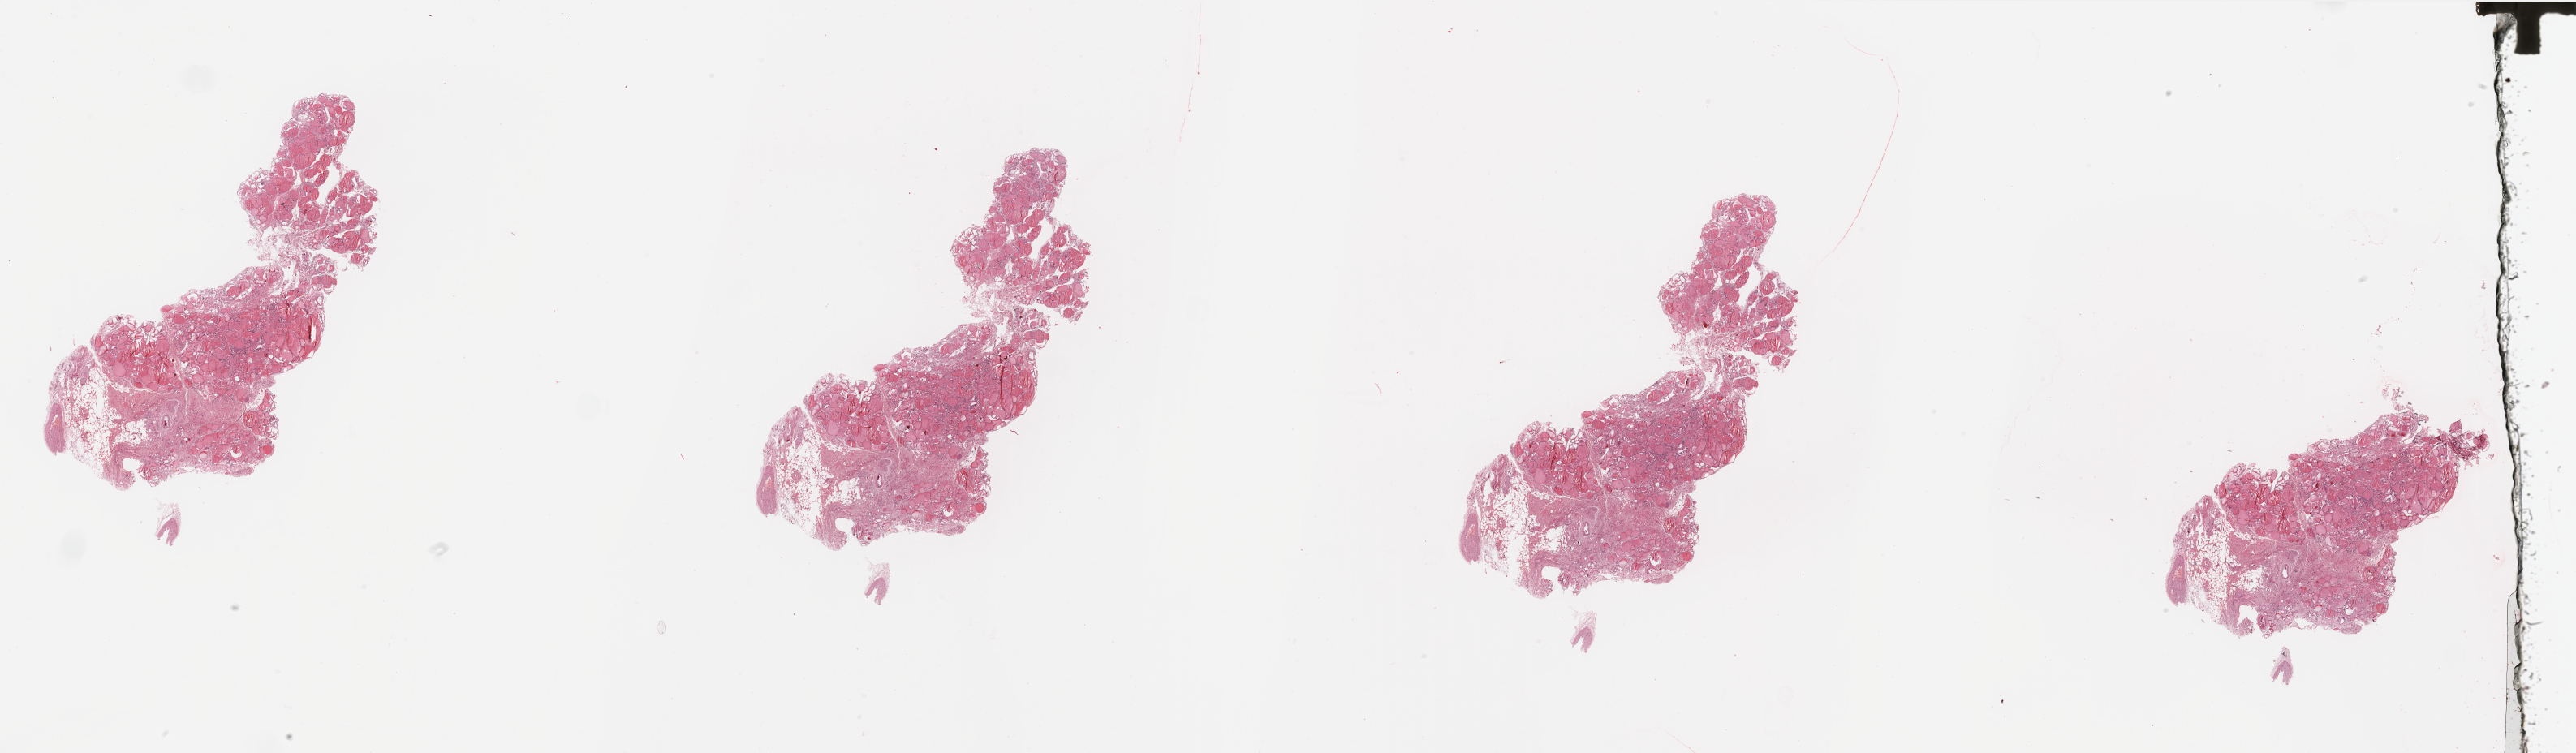
Digitized H&E tissue section (whole slide) — low-resolution overview of the scanned area, about 50.2 x 14.7 mm (slide scanned at 20x), head and neck, tissue type not recorded. 81-year-old male patient.
Patient diagnosis: Squamous cell carcinoma, NOS (larynx, NOS).